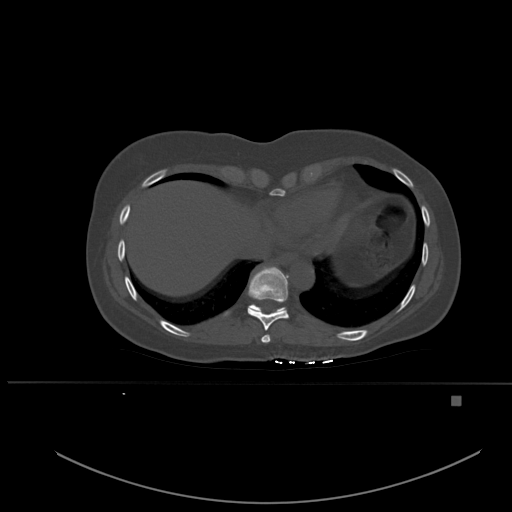
CT including the spine, one axial slice; position 302 of 651 along the scan axis; bone window (W 1800 / L 400 HU); 1.5 mm slice thickness; 512 × 512 image matrix, field of view 443 × 443 mm. Patient: female, 49 years. From the clinical record (not read from this slice): primary cancer: breast; vertebrae with lytic lesions (as recorded): L3, T12, L4.
Outlined on this slice (semi-automatically segmented with operator editing):
- T10 vertebra: bounding box (x1, y1, x2, y2) in pixels: (249, 301, 286, 314)
- T8 vertebra: (261, 334, 271, 343)
- T9 vertebra: (247, 266, 289, 331)